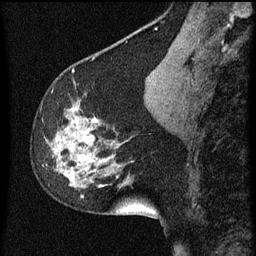
Breast MRI (dynamic contrast-enhanced), one sagittal slice. Position 25 of 60 along the scan axis. Dynamic contrast-enhanced series, image 2 of 3 at this slice position (ordered by acquisition). 1.5 T. TE 4.2 ms, TR 8 ms. 256 × 256 image matrix, field of view 180 × 180 mm. Female patient, age 61 years.
Outlined on this slice (semi-automatically segmented with operator editing):
- analysis volume of interest (the breast-tissue region the enhancement analysis was run in; not a lesion): bounding box (x1, y1, x2, y2) in pixels: (43, 82, 139, 209)
- tumour enhancement mask (voxels above the 70 % enhancement threshold inside the analysis volume of interest): (71, 172, 73, 175)